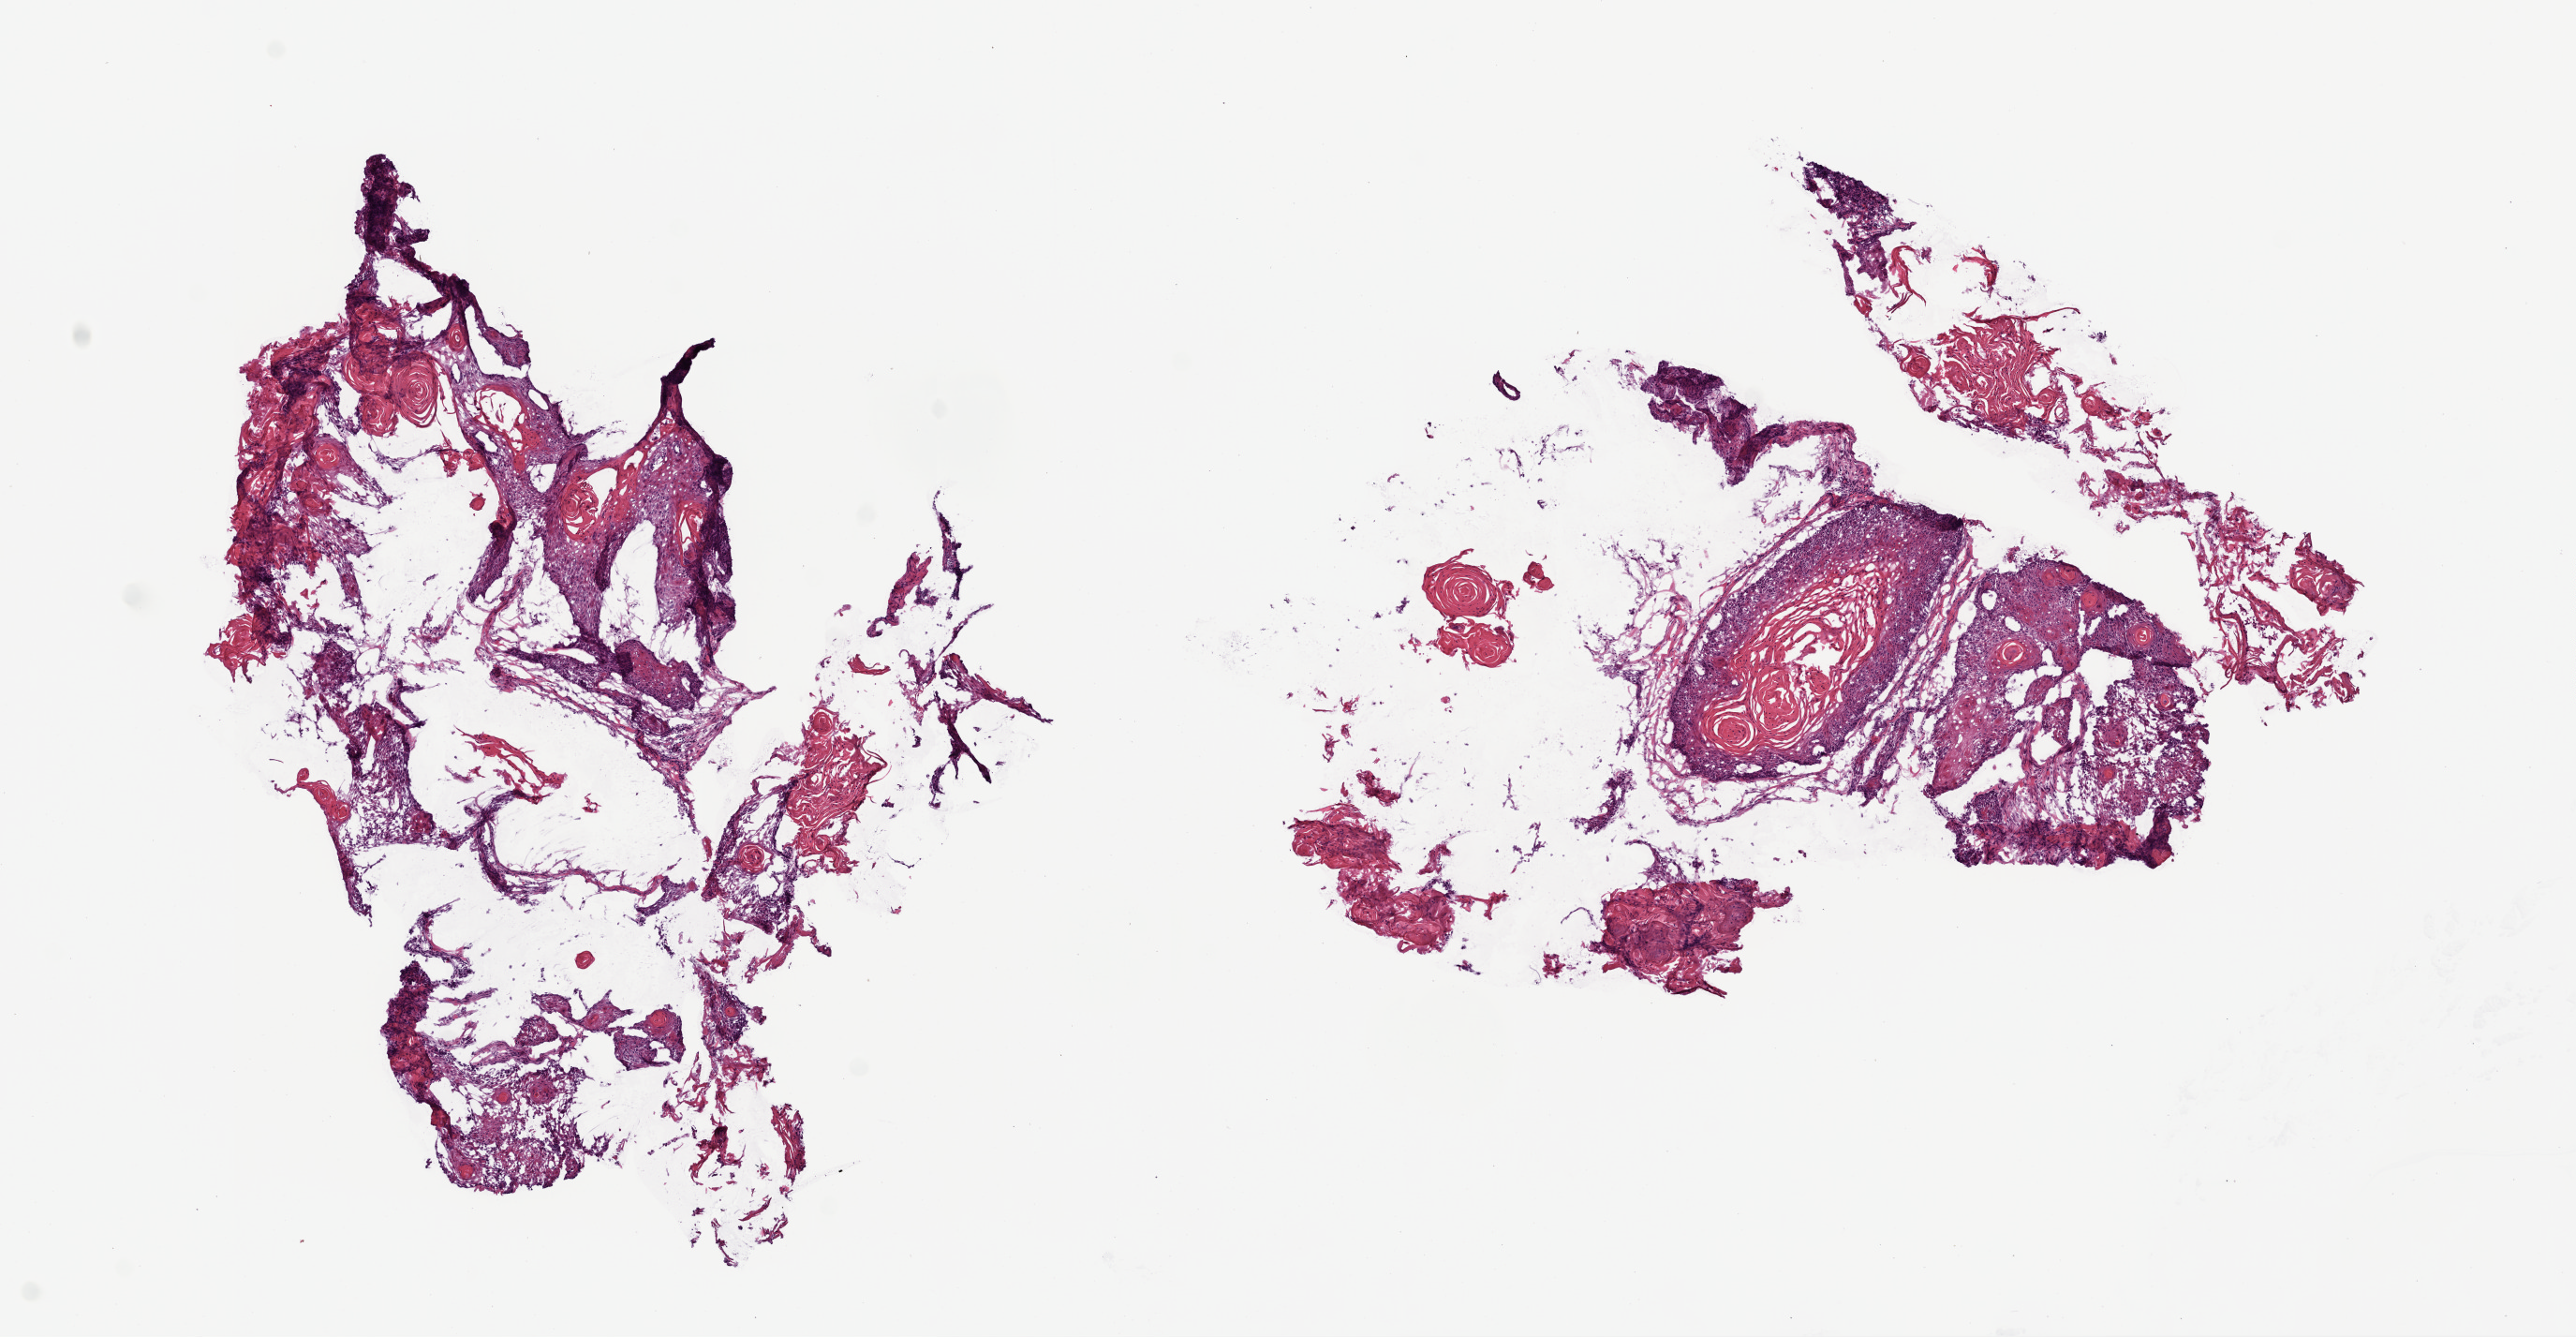
H&E whole-slide image — low-resolution overview of the scanned area, about 11.0 x 5.7 mm (from a 20x scan); frozen section from the top of the tissue portion; head and neck, primary tumour sample. Patient: male, age at initial diagnosis 62 years. Histologic grade: G2 (moderately differentiated). Slide review estimates, as recorded: tumour cells 90%, tumour nuclei 90%, normal cells 0%, stromal cells 10%, necrosis 0%.
Pathologic diagnosis: Squamous cell carcinoma, NOS (base of tongue, NOS). AJCC pathologic stage: IVA (7th edition). TNM: T3 N2b.